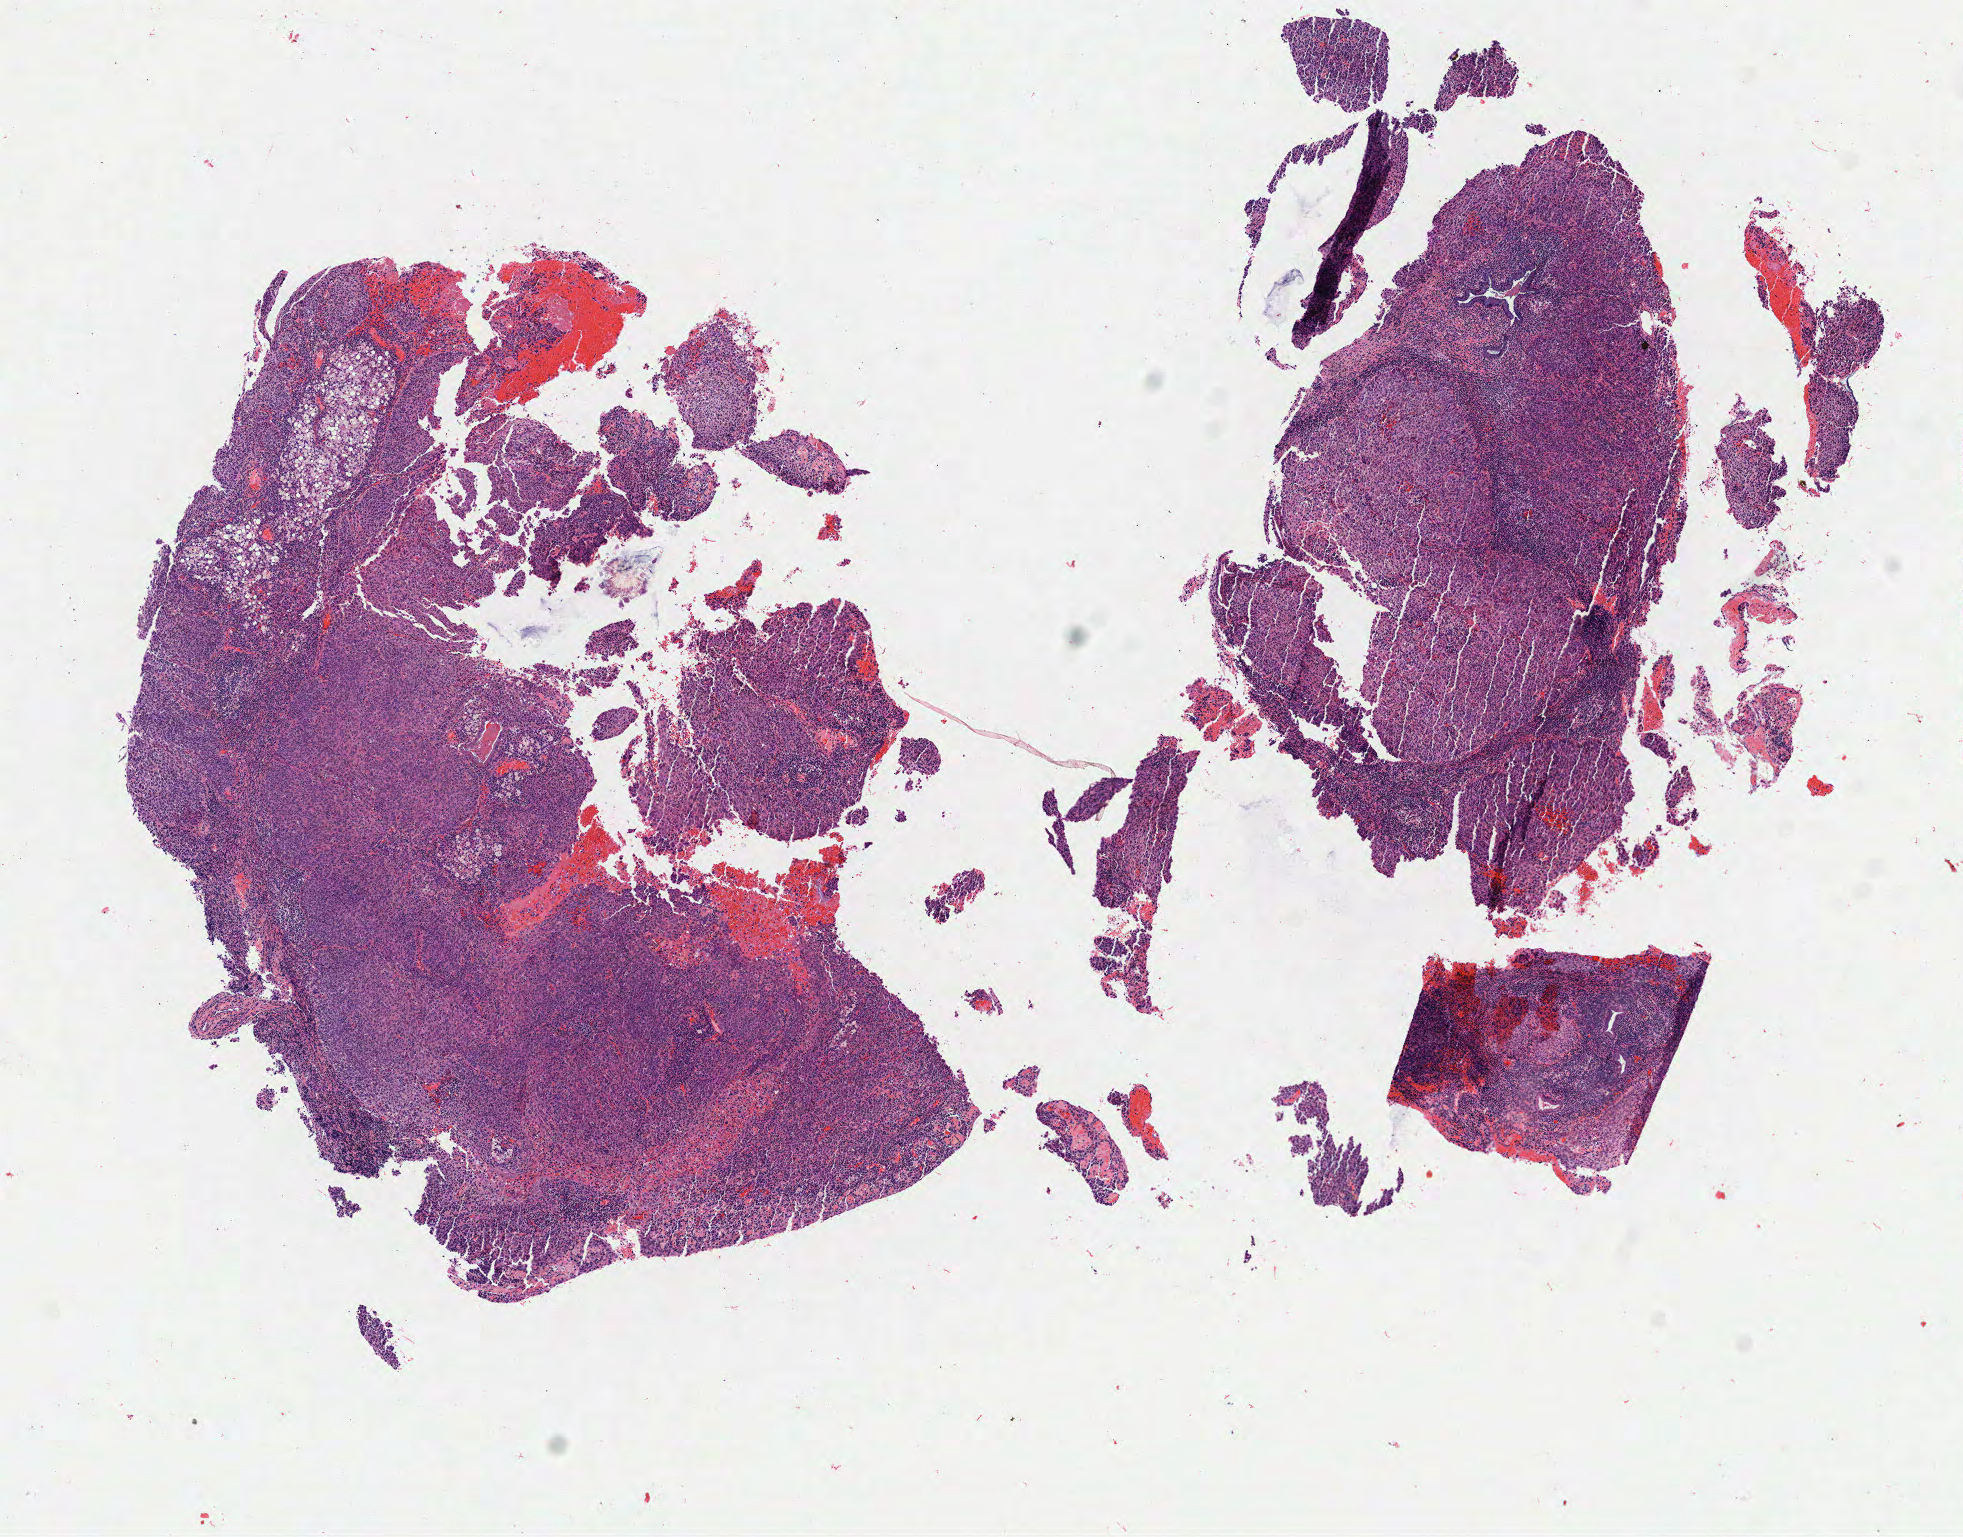
H&E whole-slide image, low-resolution overview of the scanned area, about 7.8 x 6.1 mm. Tumor tissue. Anatomic site: cervix. Female patient, age 62 years.
Histologic diagnosis: Squamous cell carcinoma, large cell, nonkeratinizing, NOS.